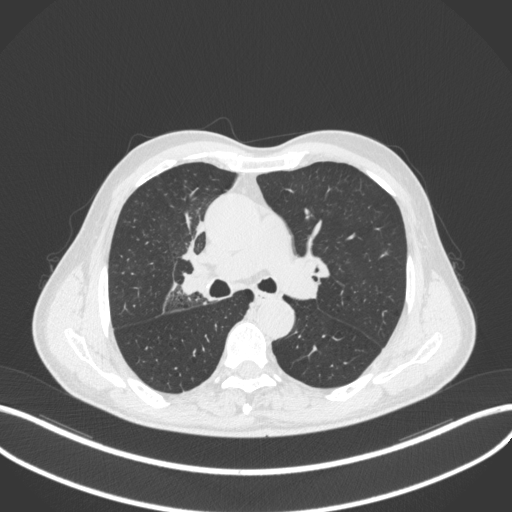
Chest CT, one axial slice. 120 kVp. Lung window (W 1500 / L -600 HU). 1 mm slice thickness. 512 × 512 image matrix. Patient: male, 69 years. From the clinical record (not read from this slice): clinical TNM (as recorded): T2a N0 M0.
Outlined on this slice (rectangle marked by the reading radiologist):
- lung tumour (recorded histology: adenocarcinoma): bounding box <175,264,209,302> (left, top, right, bottom; pixels)